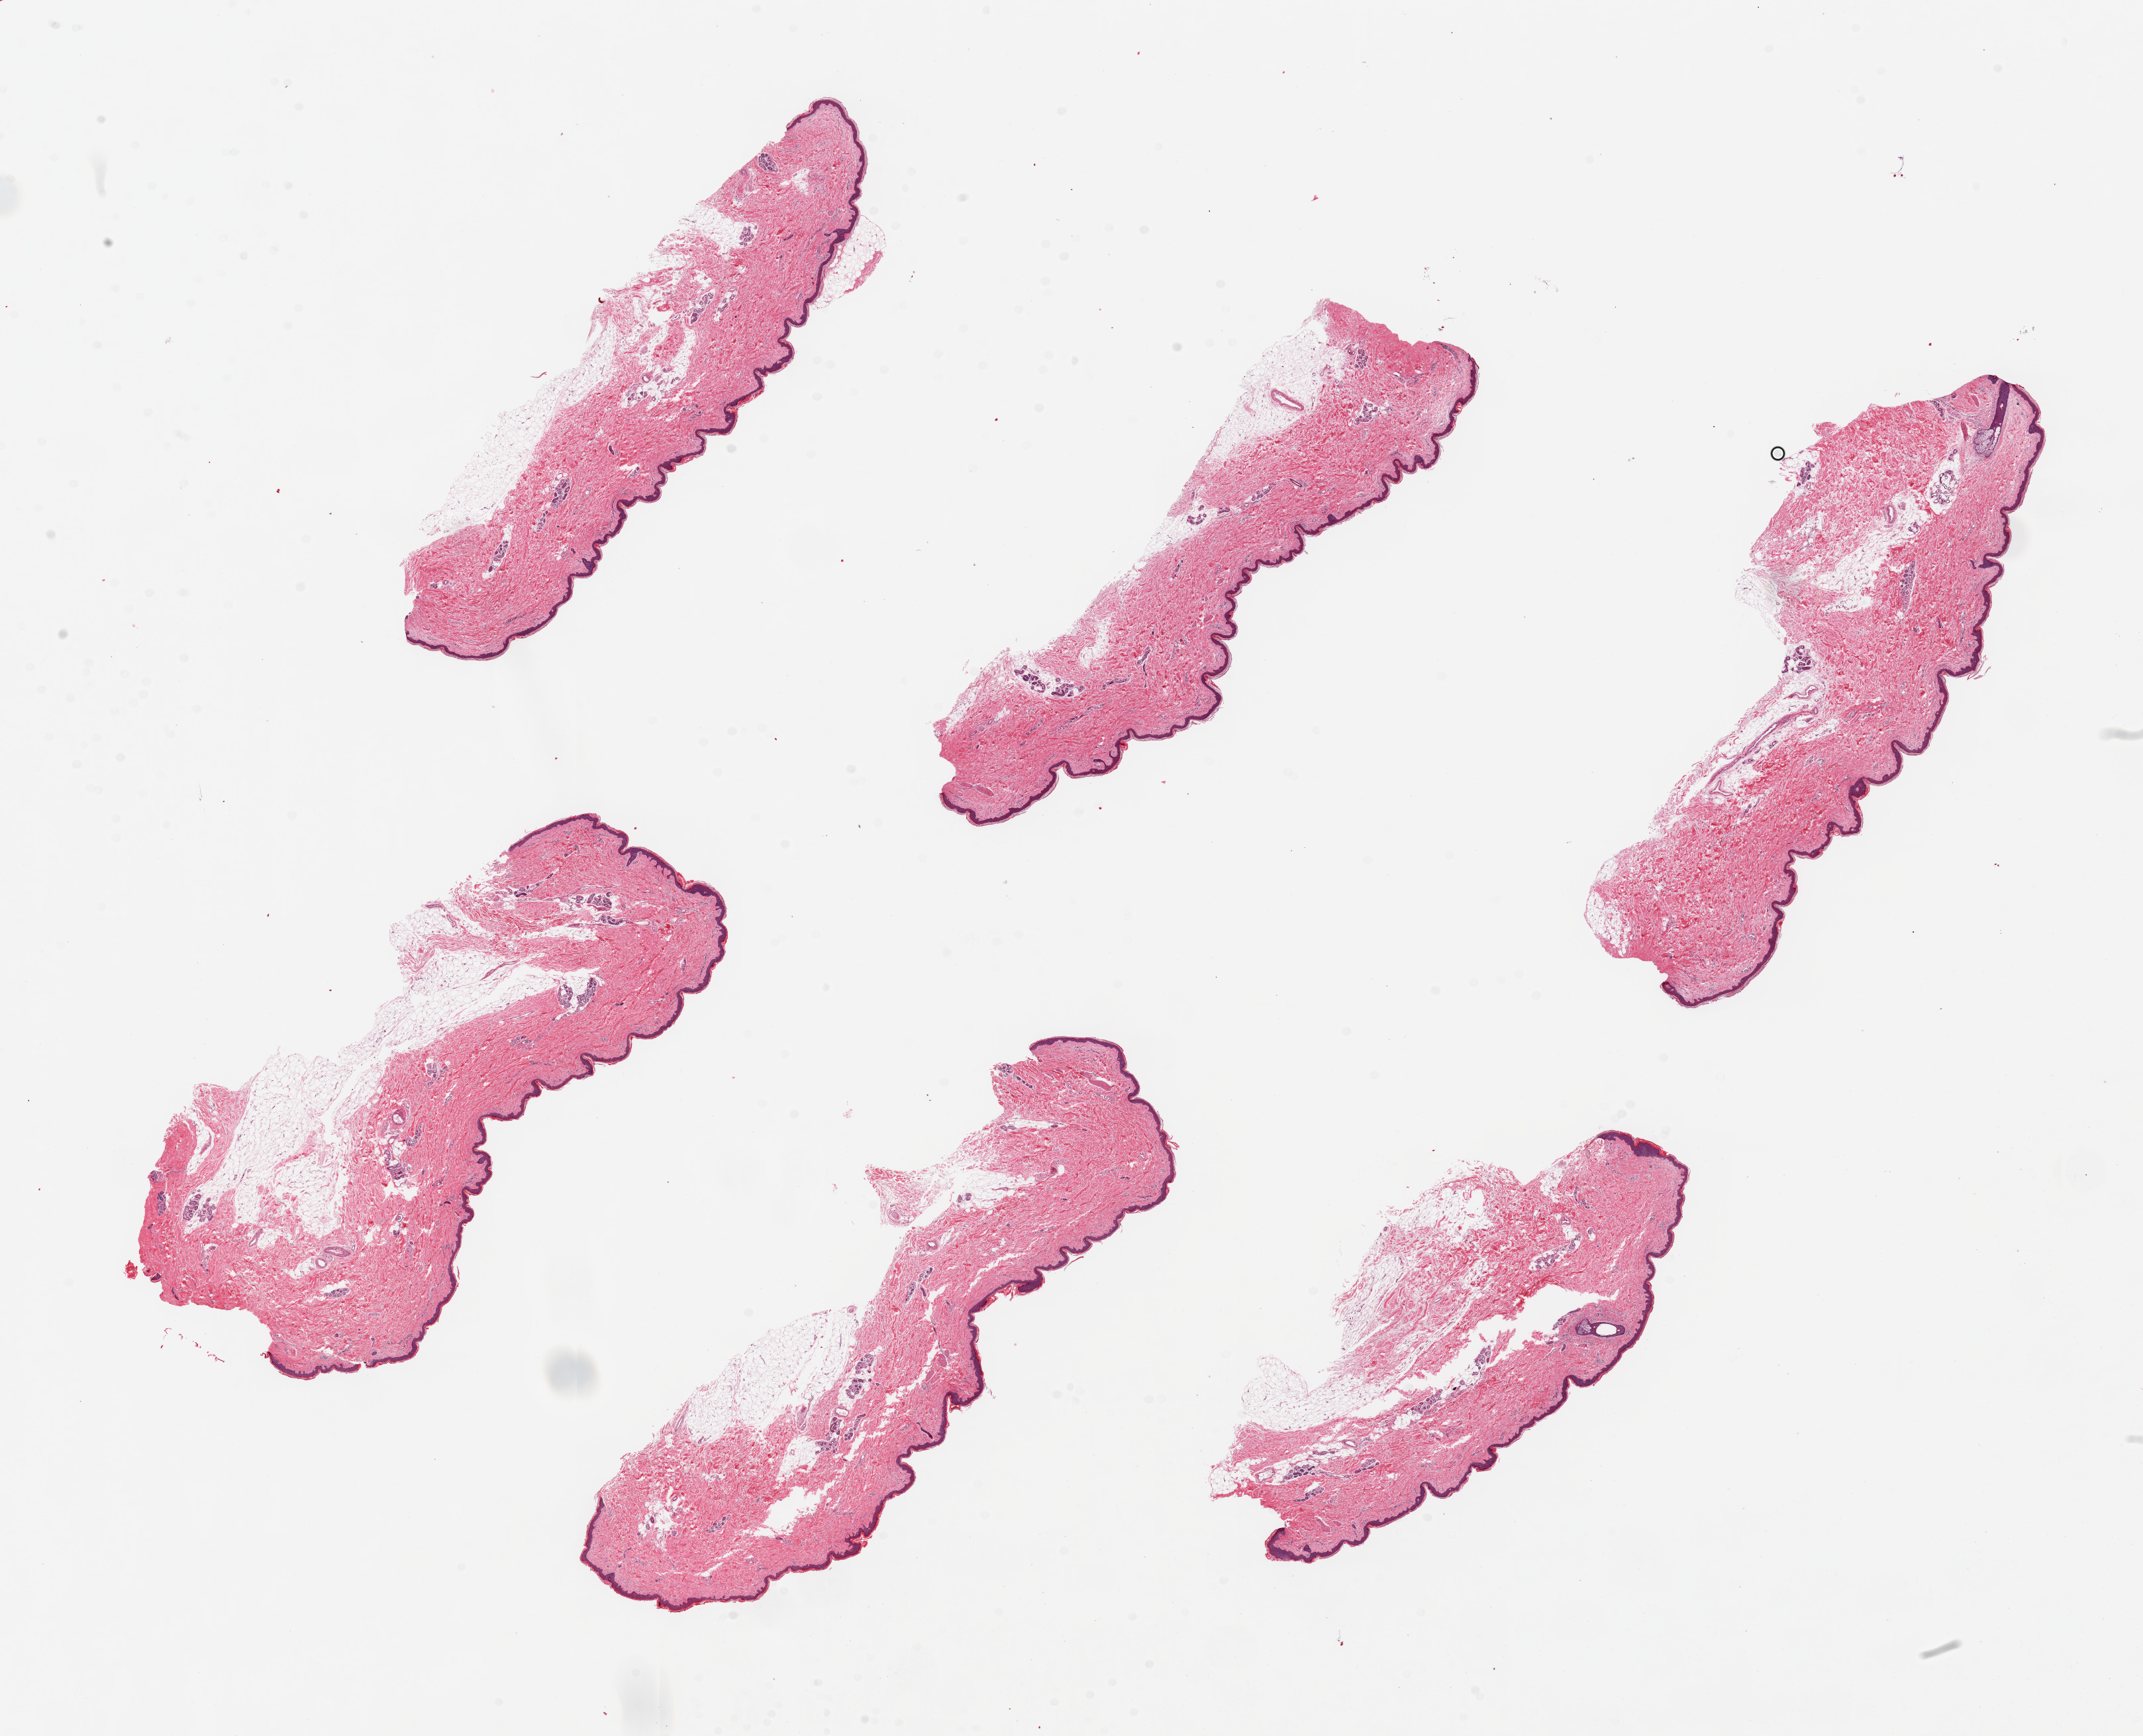
Digitized H&E-stained section — shown as a low-resolution overview of the whole scanned area (about 25.6 x 20.7 mm, acquisition: 20x scan), PAXgene-fixed paraffin-embedded (PFPE) section, target tissue: skin of lower leg, donor tissue sample. Donor: male.
• pathologist's review note for this sample: 6 pieces ~8x2mm. Squamous epithelium is ~2-3% of thickness